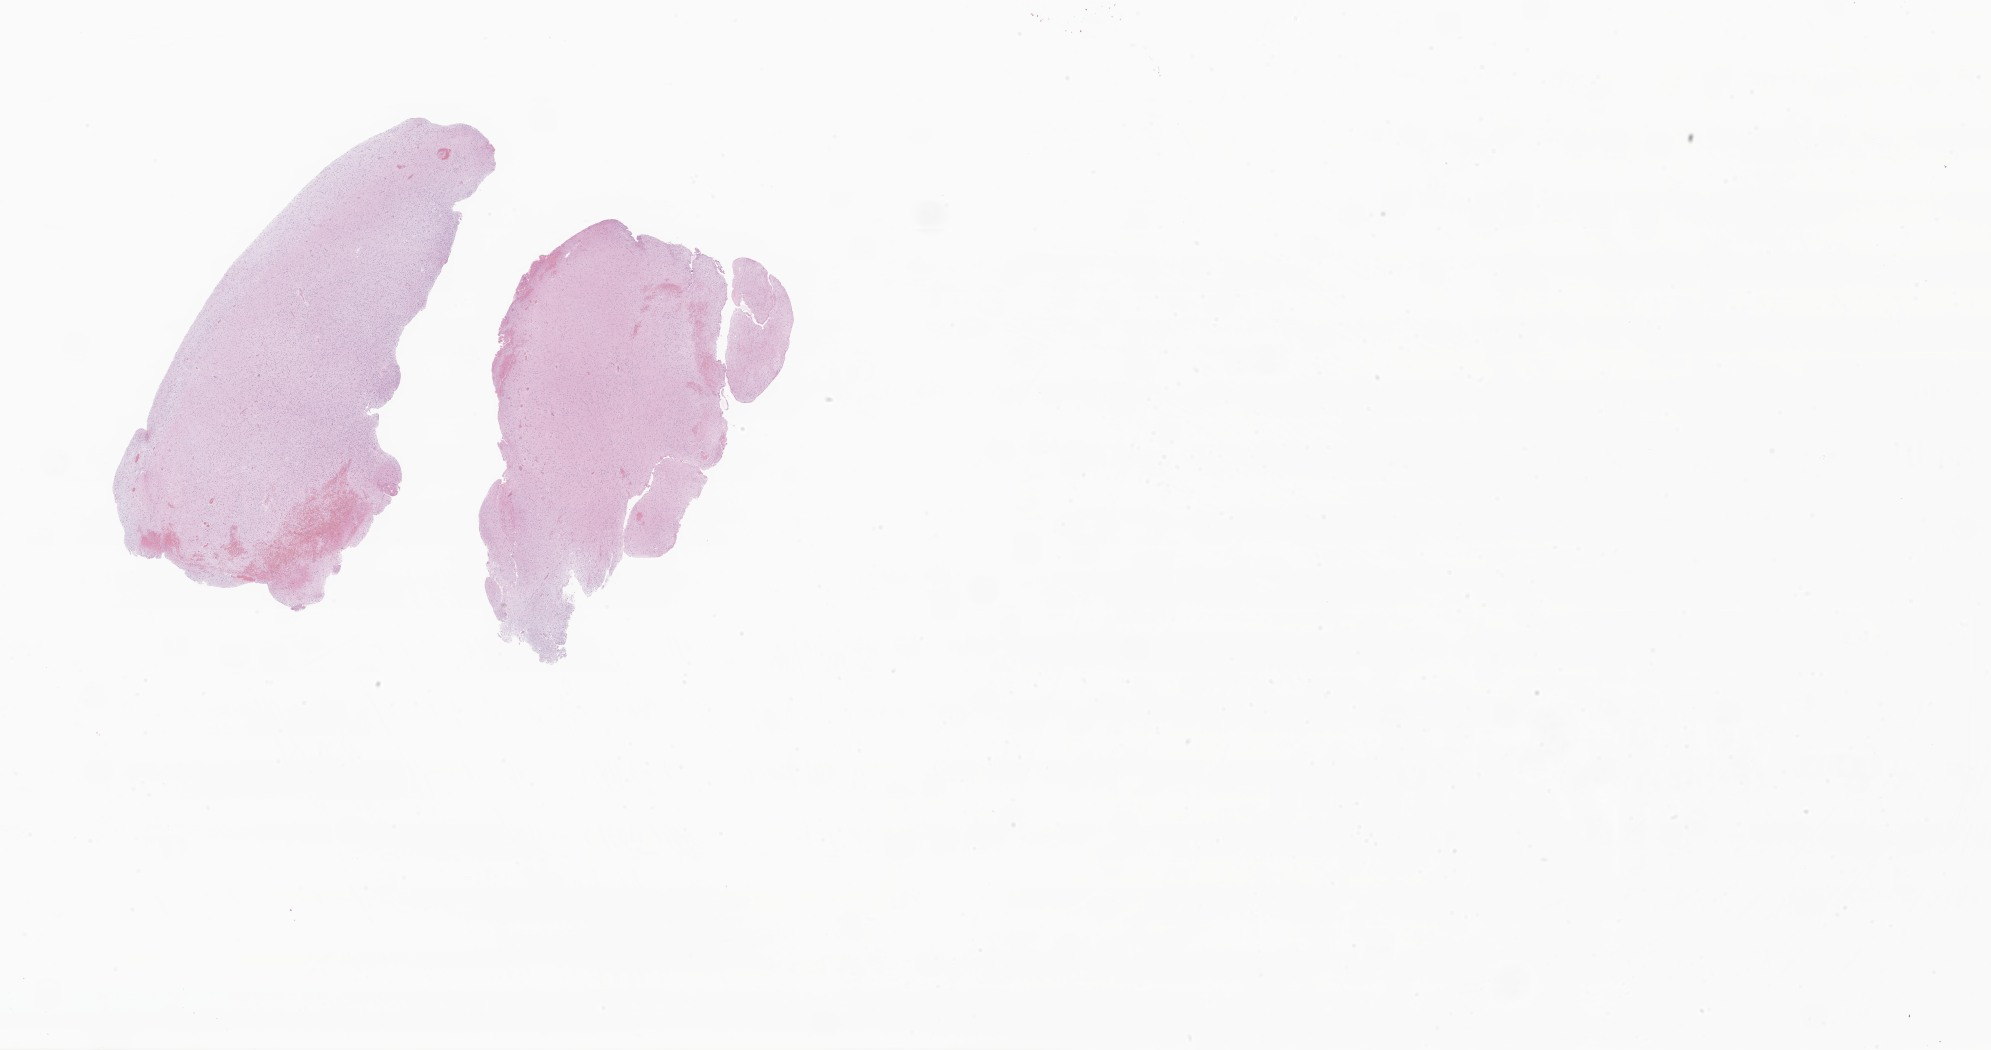
Whole-slide image, haematoxylin and eosin stain of tumor tissue from the brain, whole scanned area (about 33.6 x 17.7 mm) shown as a low-resolution overview, FFPE section. Patient female; age 242 months.
Recorded diagnosis: Neoplasm, uncertain whether benign or malignant.